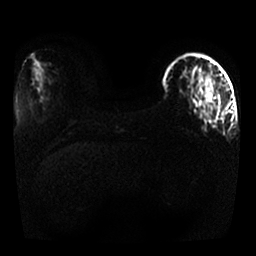
Breast MRI, one axial slice. Position 9 of 25 along the scan axis. Diffusion-weighted series; image 2 of 4 stored at this slice position (different b-values; order by instance number). 1.5 T. 4 mm slice thickness. 256 × 256 image matrix, field of view 330 × 330 mm. Female patient.
Outlined on this slice (manually delineated by an expert):
- tumour on diffusion-weighted imaging: bounding box [x1, y1, x2, y2] px = [205, 93, 212, 101]